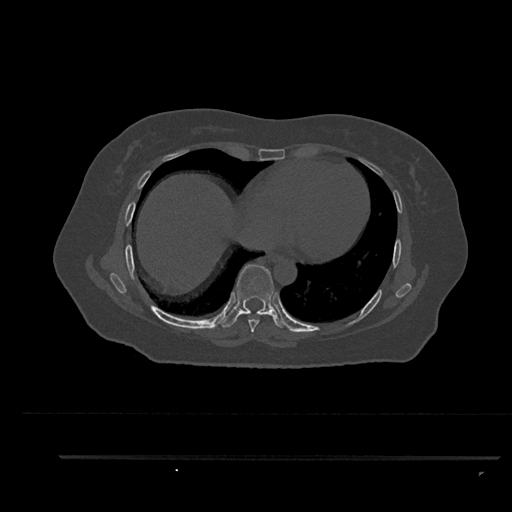
CT including the spine, one axial slice. Slice 478 of 797 in the series (ordered by position). 120 kVp. Bone window (W 1800 / L 400 HU). 512 × 512 image matrix, field of view 408 × 408 mm. Female patient, age 44 years. Case-level facts recorded for this patient, not image findings: primary cancer: renal.
Annotated regions visible in this slice (semi-automatically segmented with operator editing):
- T7 vertebra: bounding box [x1, y1, x2, y2] px = [248, 319, 260, 333]
- T8 vertebra: [222, 264, 287, 328]